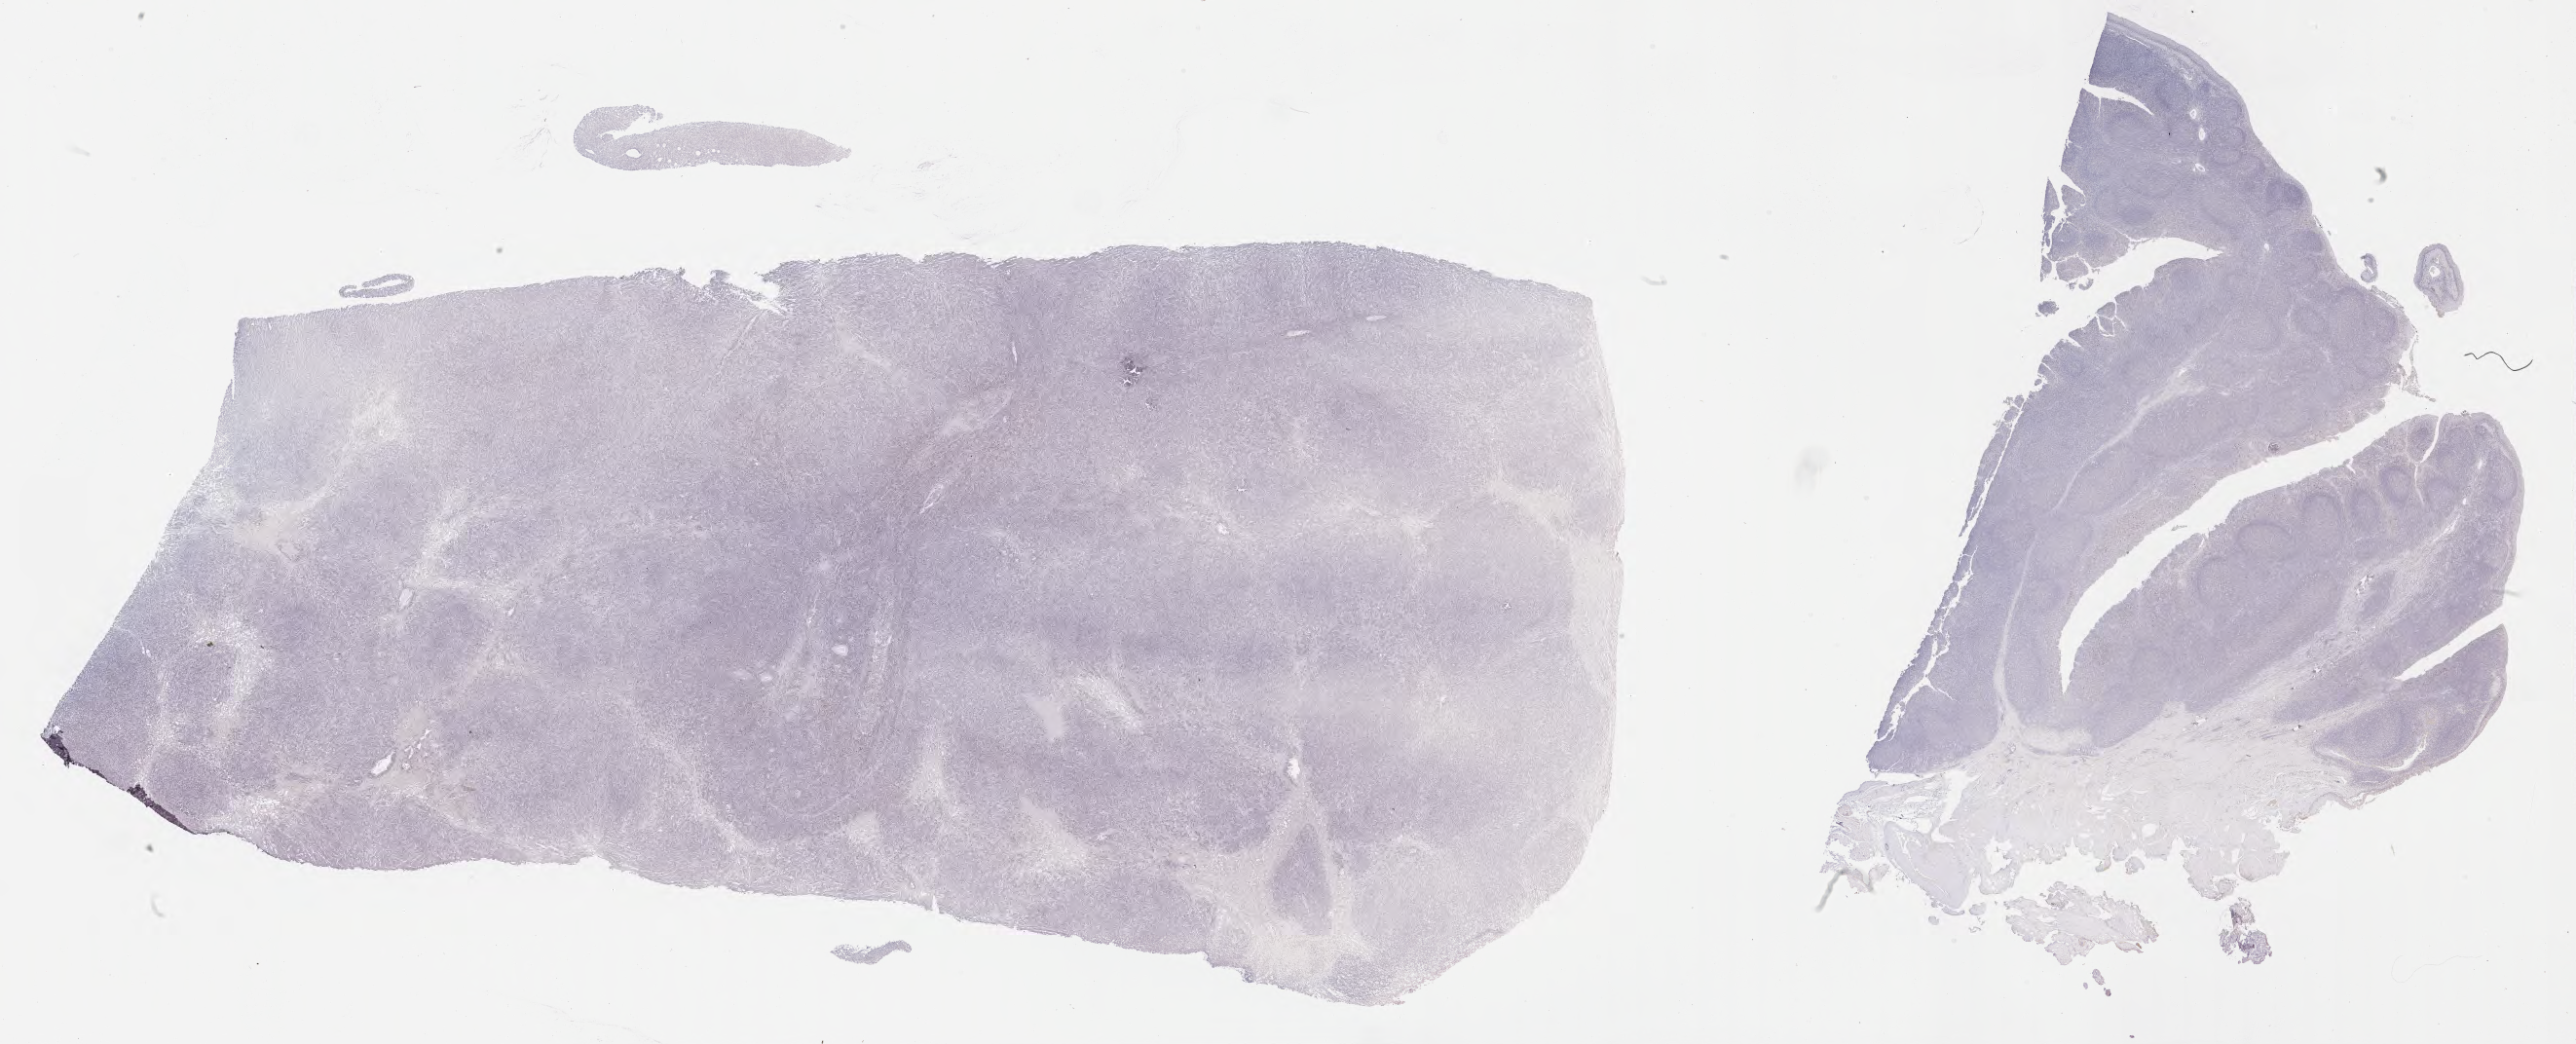
Immunohistochemistry (IHC) whole-slide image stained for p53 — whole scanned area (about 42.8 x 17.3 mm) shown as a low-resolution overview, specimen: tumor tissue. Male patient, aged 39.
Diagnosis: Diffuse large B-cell lymphoma, NOS.